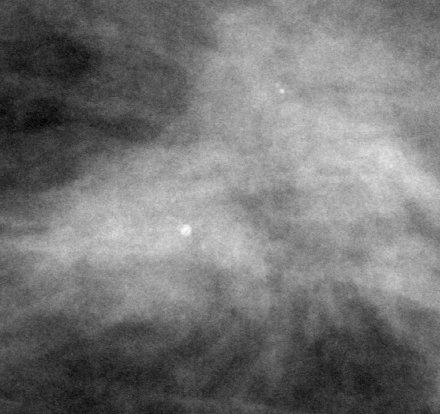
Region of interest cut from a scanned film mammogram (one marked finding), left breast, CC view.
Marked abnormality: mass, shape irregular, margins ill defined; BI-RADS assessment category 5; pathology (as recorded): malignant.